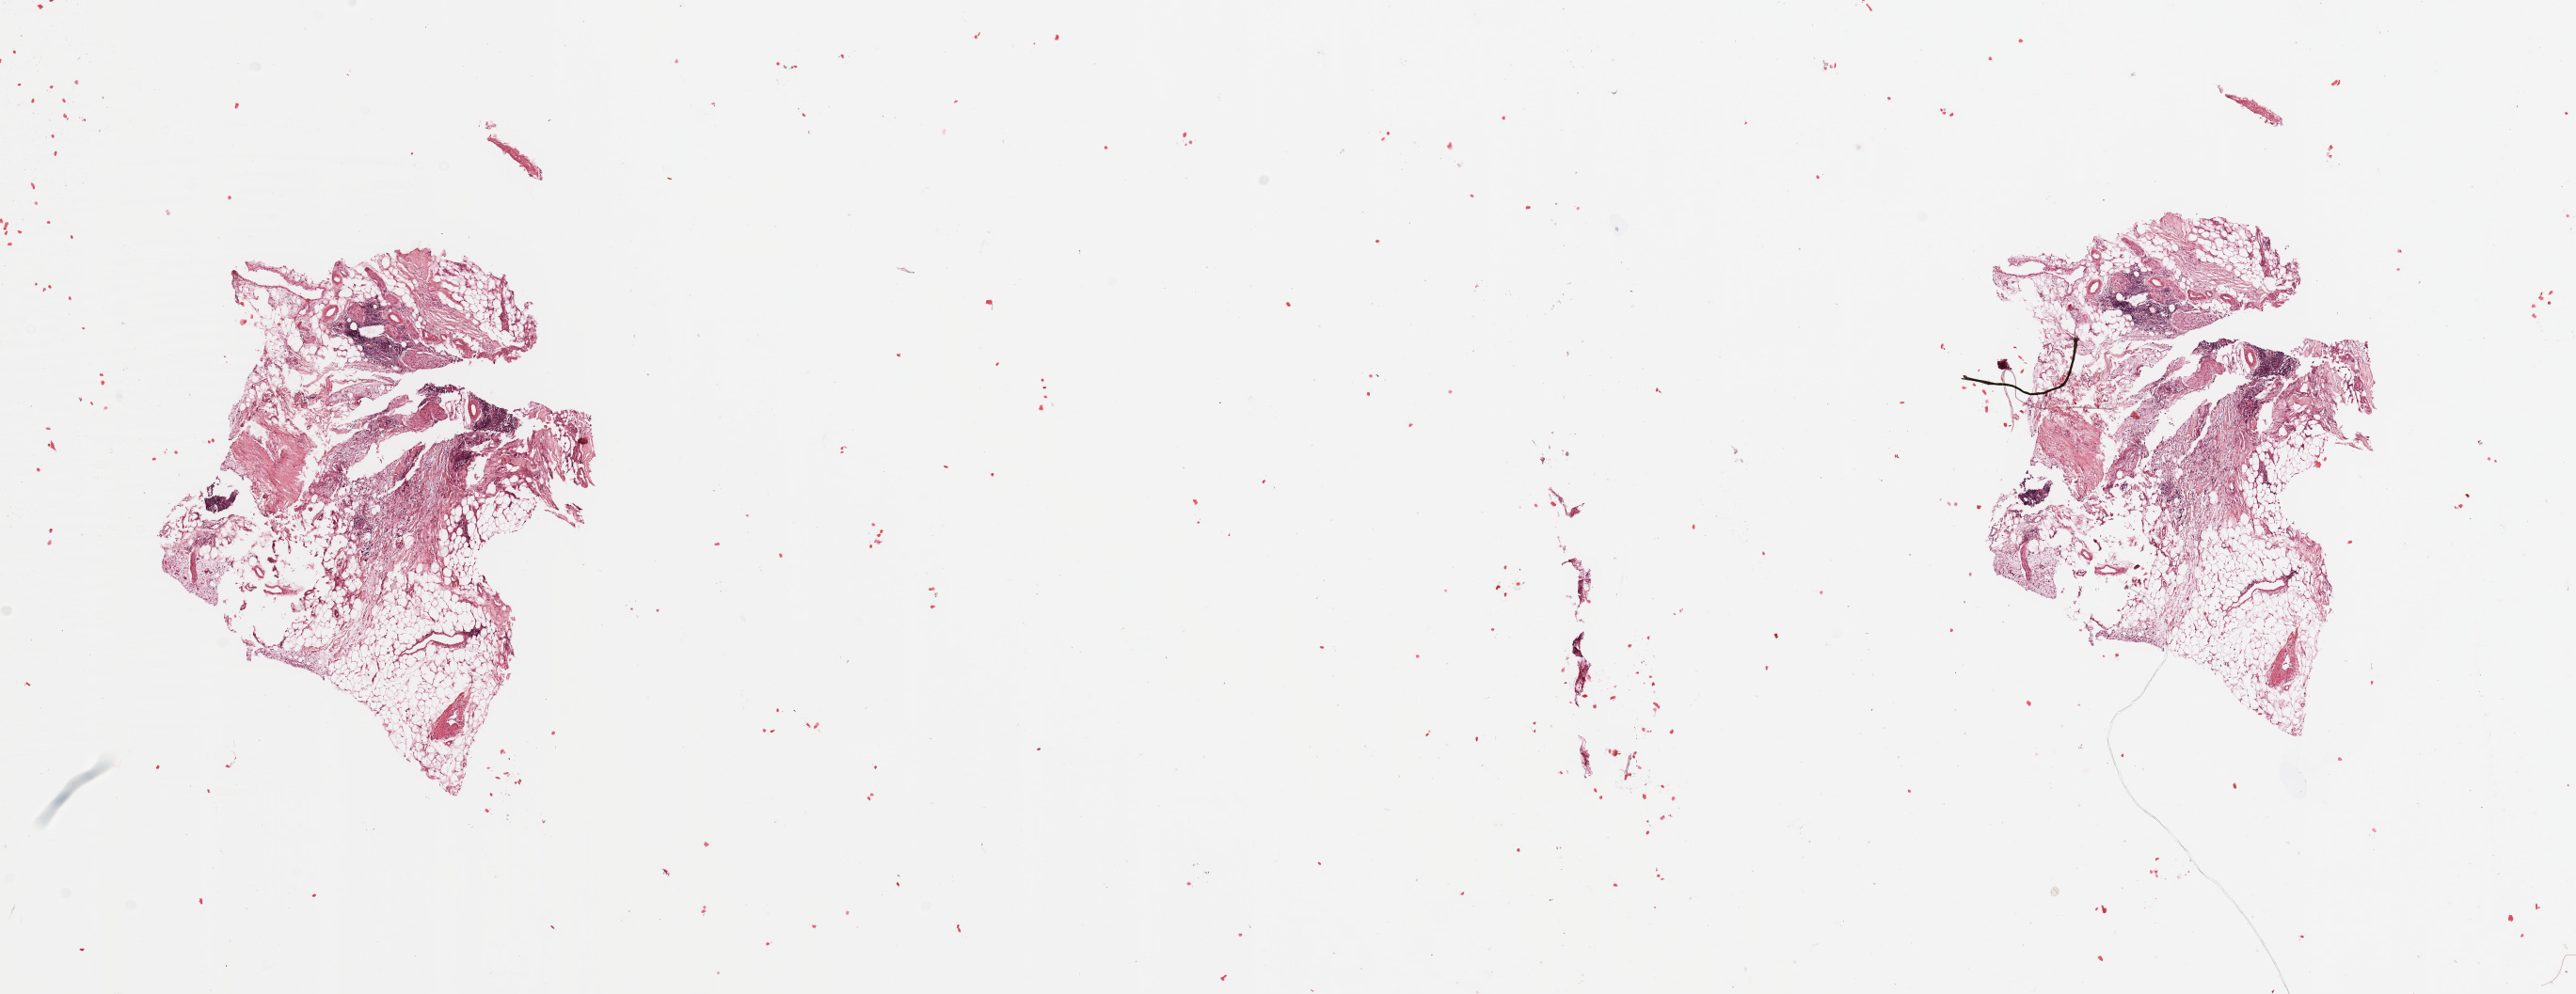
Hematoxylin and eosin (H&E) stained whole-slide image, shown as a low-resolution overview of the whole scanned area (about 21.7 x 8.4 mm, slide scanned at 20x); tumour tissue sample, pancreas. Female, 69 y/o.
Histologic diagnosis: Infiltrating duct carcinoma, NOS.